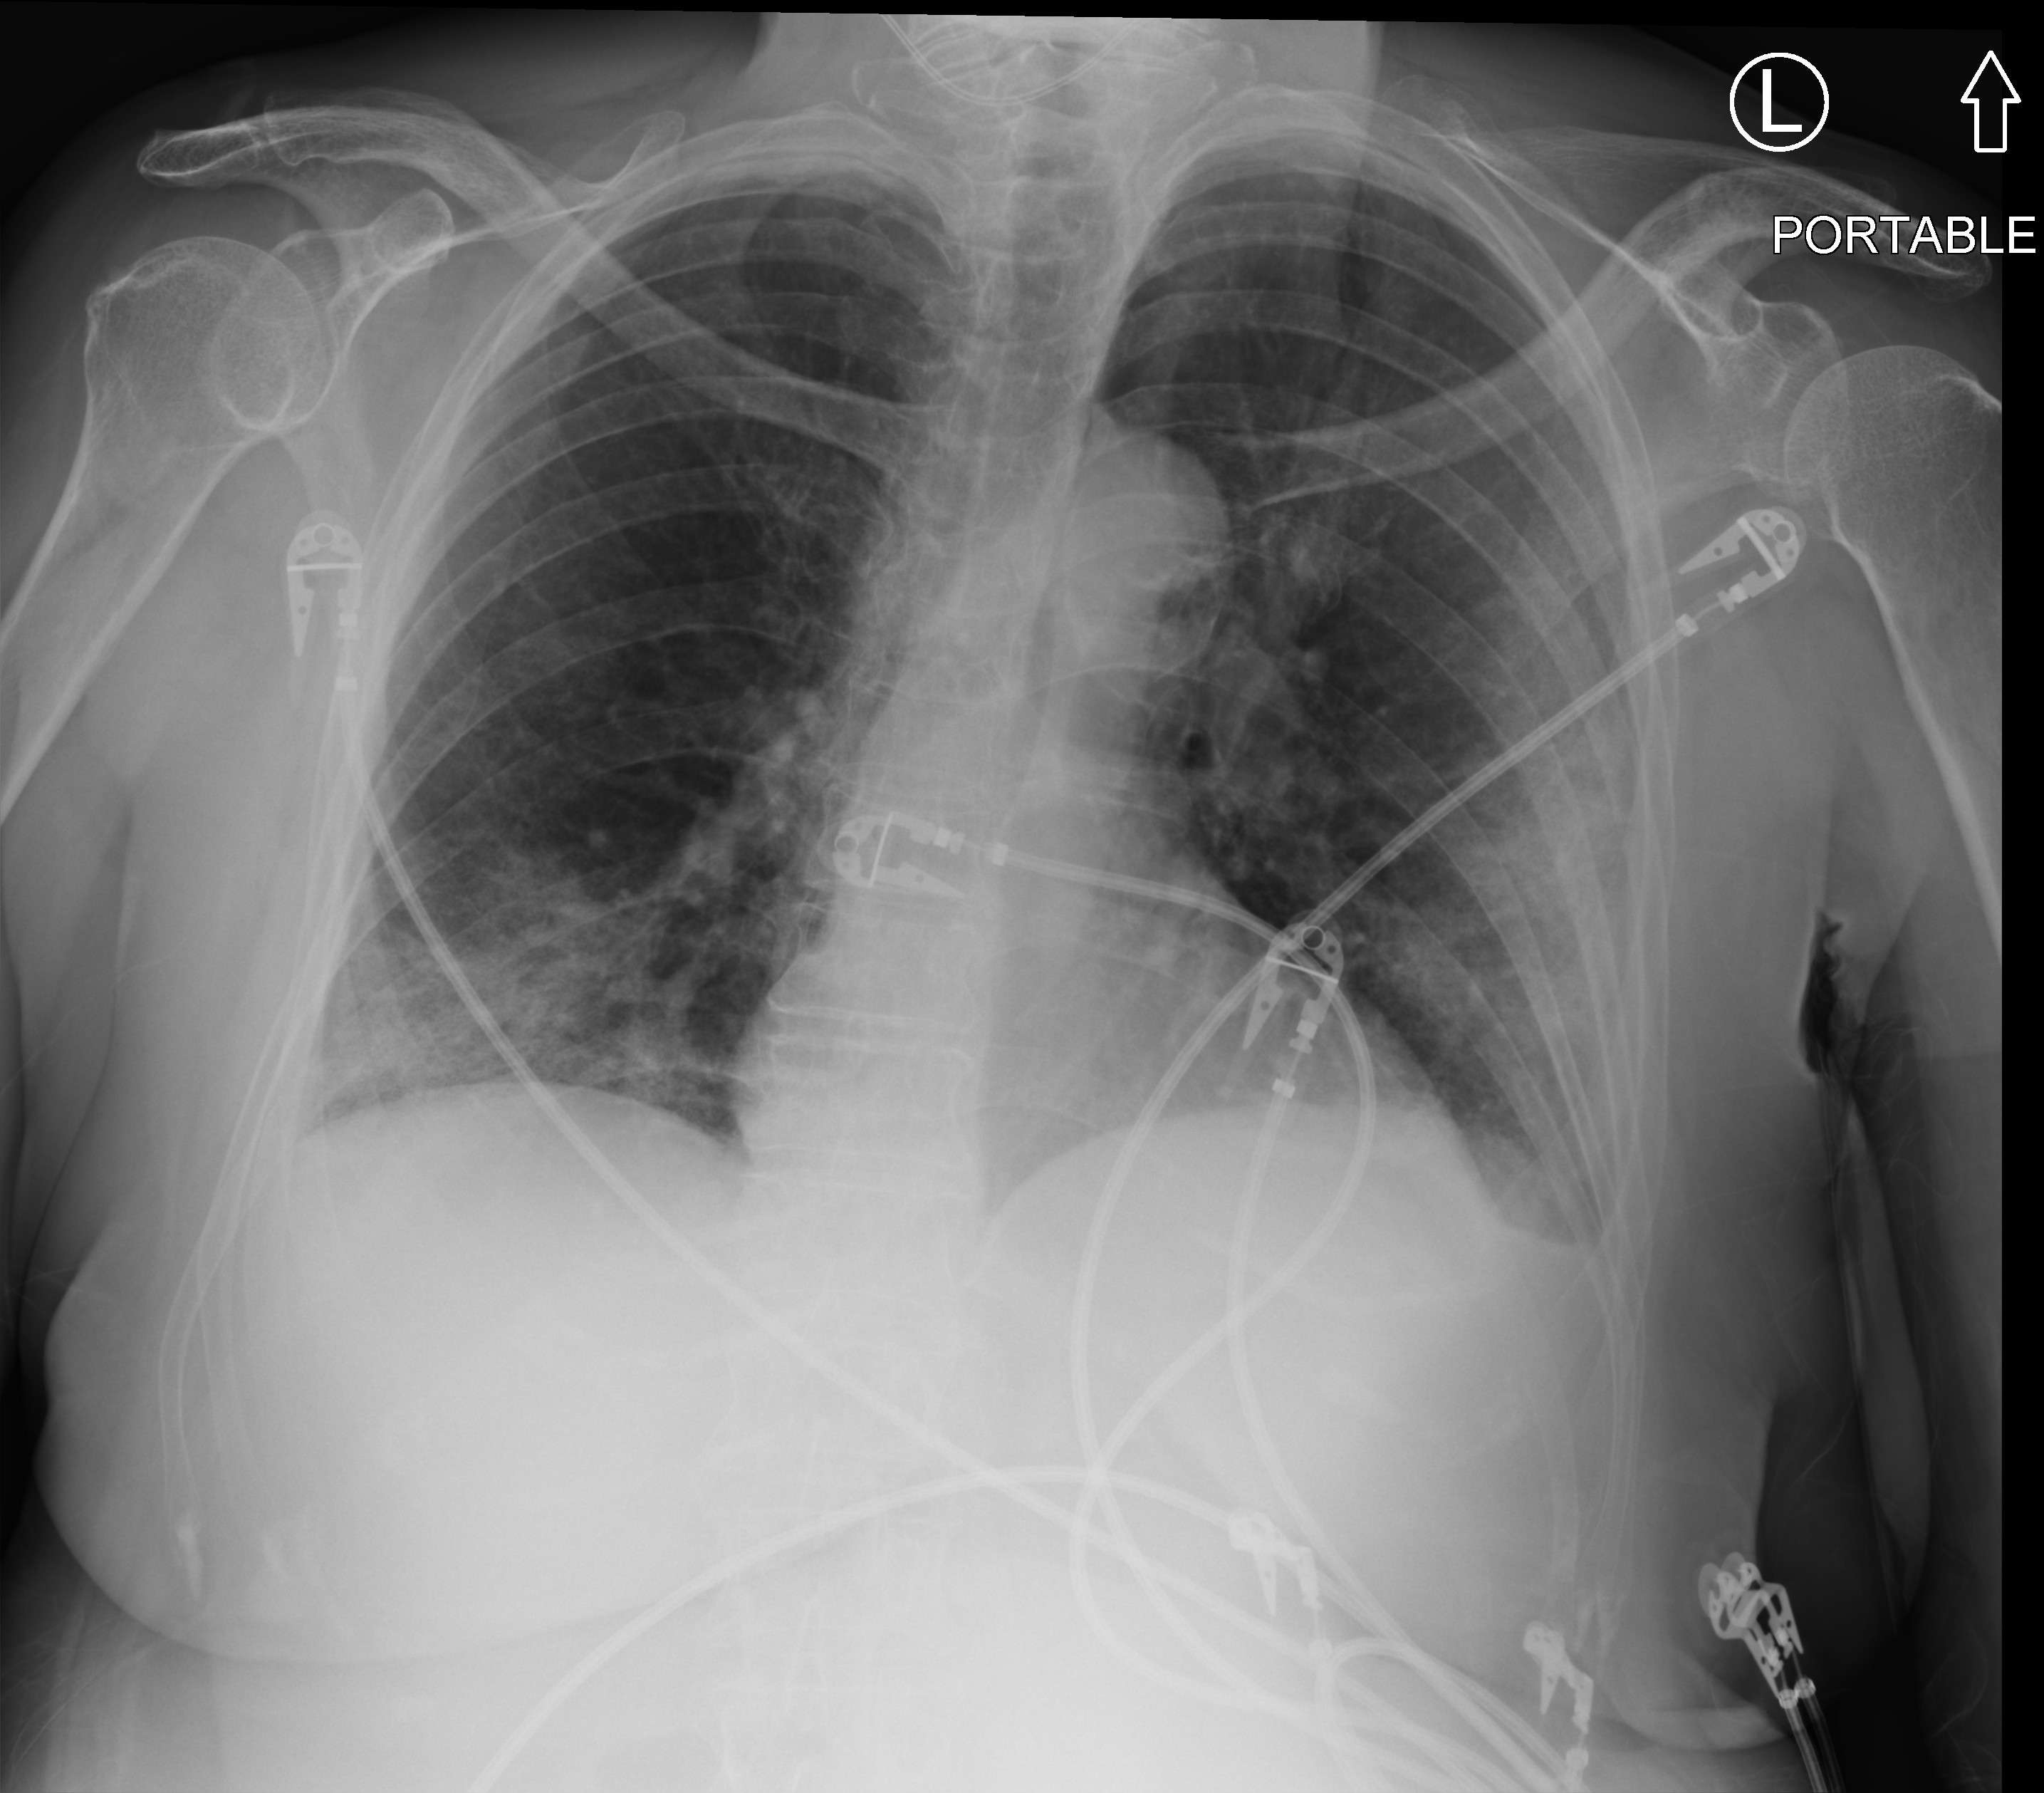
Chest X-ray (portable), anteroposterior (AP) projection. Female patient hospitalised with COVID-19, age 60–74 years.
Hospital-stay facts (about this admission, not read from this image; timing relative to this image not recorded):
- length of hospital stay: 4 days
- mechanically ventilated during this hospital stay: no
- admitted to intensive care during this hospital stay: no